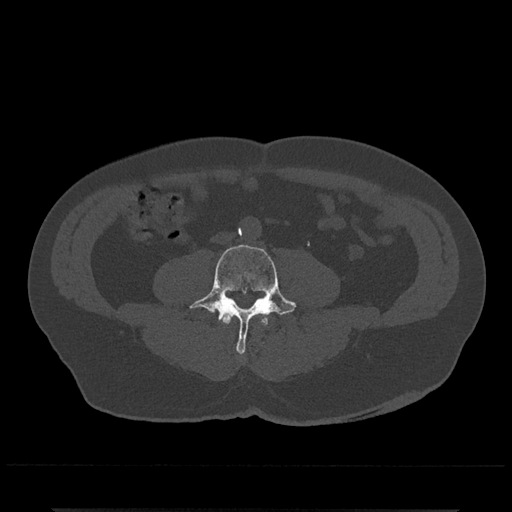
CT including the spine, one axial slice; slice 156 of 797 in the series (ordered by position); reconstruction kernel Br40s/3; 120 kVp; bone window (W 1800 / L 400 HU); 0.5 mm slice thickness; 512 × 512 image matrix, field of view 393 × 393 mm. Male patient, age 67 years. Case-level facts recorded for this patient, not image findings: primary cancer: prostate.
Structures marked on this image (semi-automatic segmentation, software-assisted and operator-edited):
- L3 vertebra: bounding box (x1, y1, x2, y2) in pixels: (220, 312, 269, 326)
- L4 vertebra: (189, 244, 297, 354)